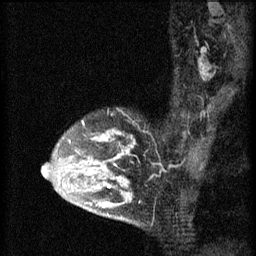
Breast MRI (dynamic contrast-enhanced), one sagittal slice; slice 45 of 60 in the series (ordered by position); 3 images stored at this slice position (order not interpretable as contrast timing); 1.5 T; TE 4.2 ms, TR 8.2 ms; 256 × 256 image matrix, field of view 180 × 180 mm. Patient: female, 45 years.
Structures marked on this image (semi-automatic segmentation, software-assisted and operator-edited):
- analysis volume of interest (the breast-tissue region the enhancement analysis was run in; not a lesion): bounding box [x1, y1, x2, y2] px = [54, 120, 141, 217]
- tumour enhancement mask (voxels above the 70 % enhancement threshold inside the analysis volume of interest): [68, 120, 133, 209]